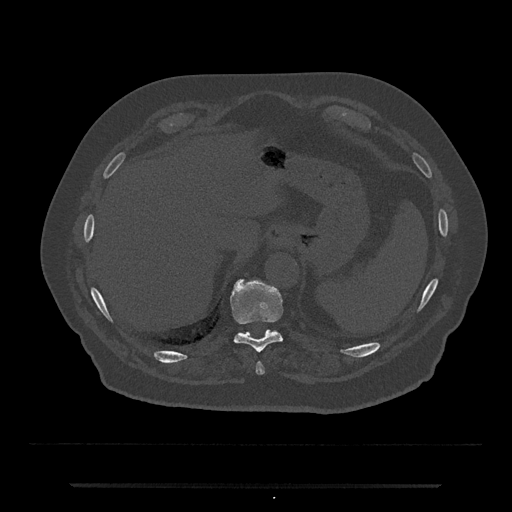
CT including the spine, one axial slice; slice 700 of 797 in the series (ordered by position); bone window (W 1800 / L 400 HU); 0.5 mm slice thickness; 512 × 512 image matrix. Patient: male, 80 years. Case-level facts recorded for this patient, not image findings: primary cancer: prostate; vertebrae with lytic lesions (as recorded): L1, T11.
Annotated regions visible in this slice (semi-automatic segmentation, software-assisted and operator-edited):
- T10 vertebra: bounding box <230,279,283,353> (left, top, right, bottom; pixels)
- T11 vertebra: <271,330,277,332>
- T9 vertebra: <256,362,265,375>